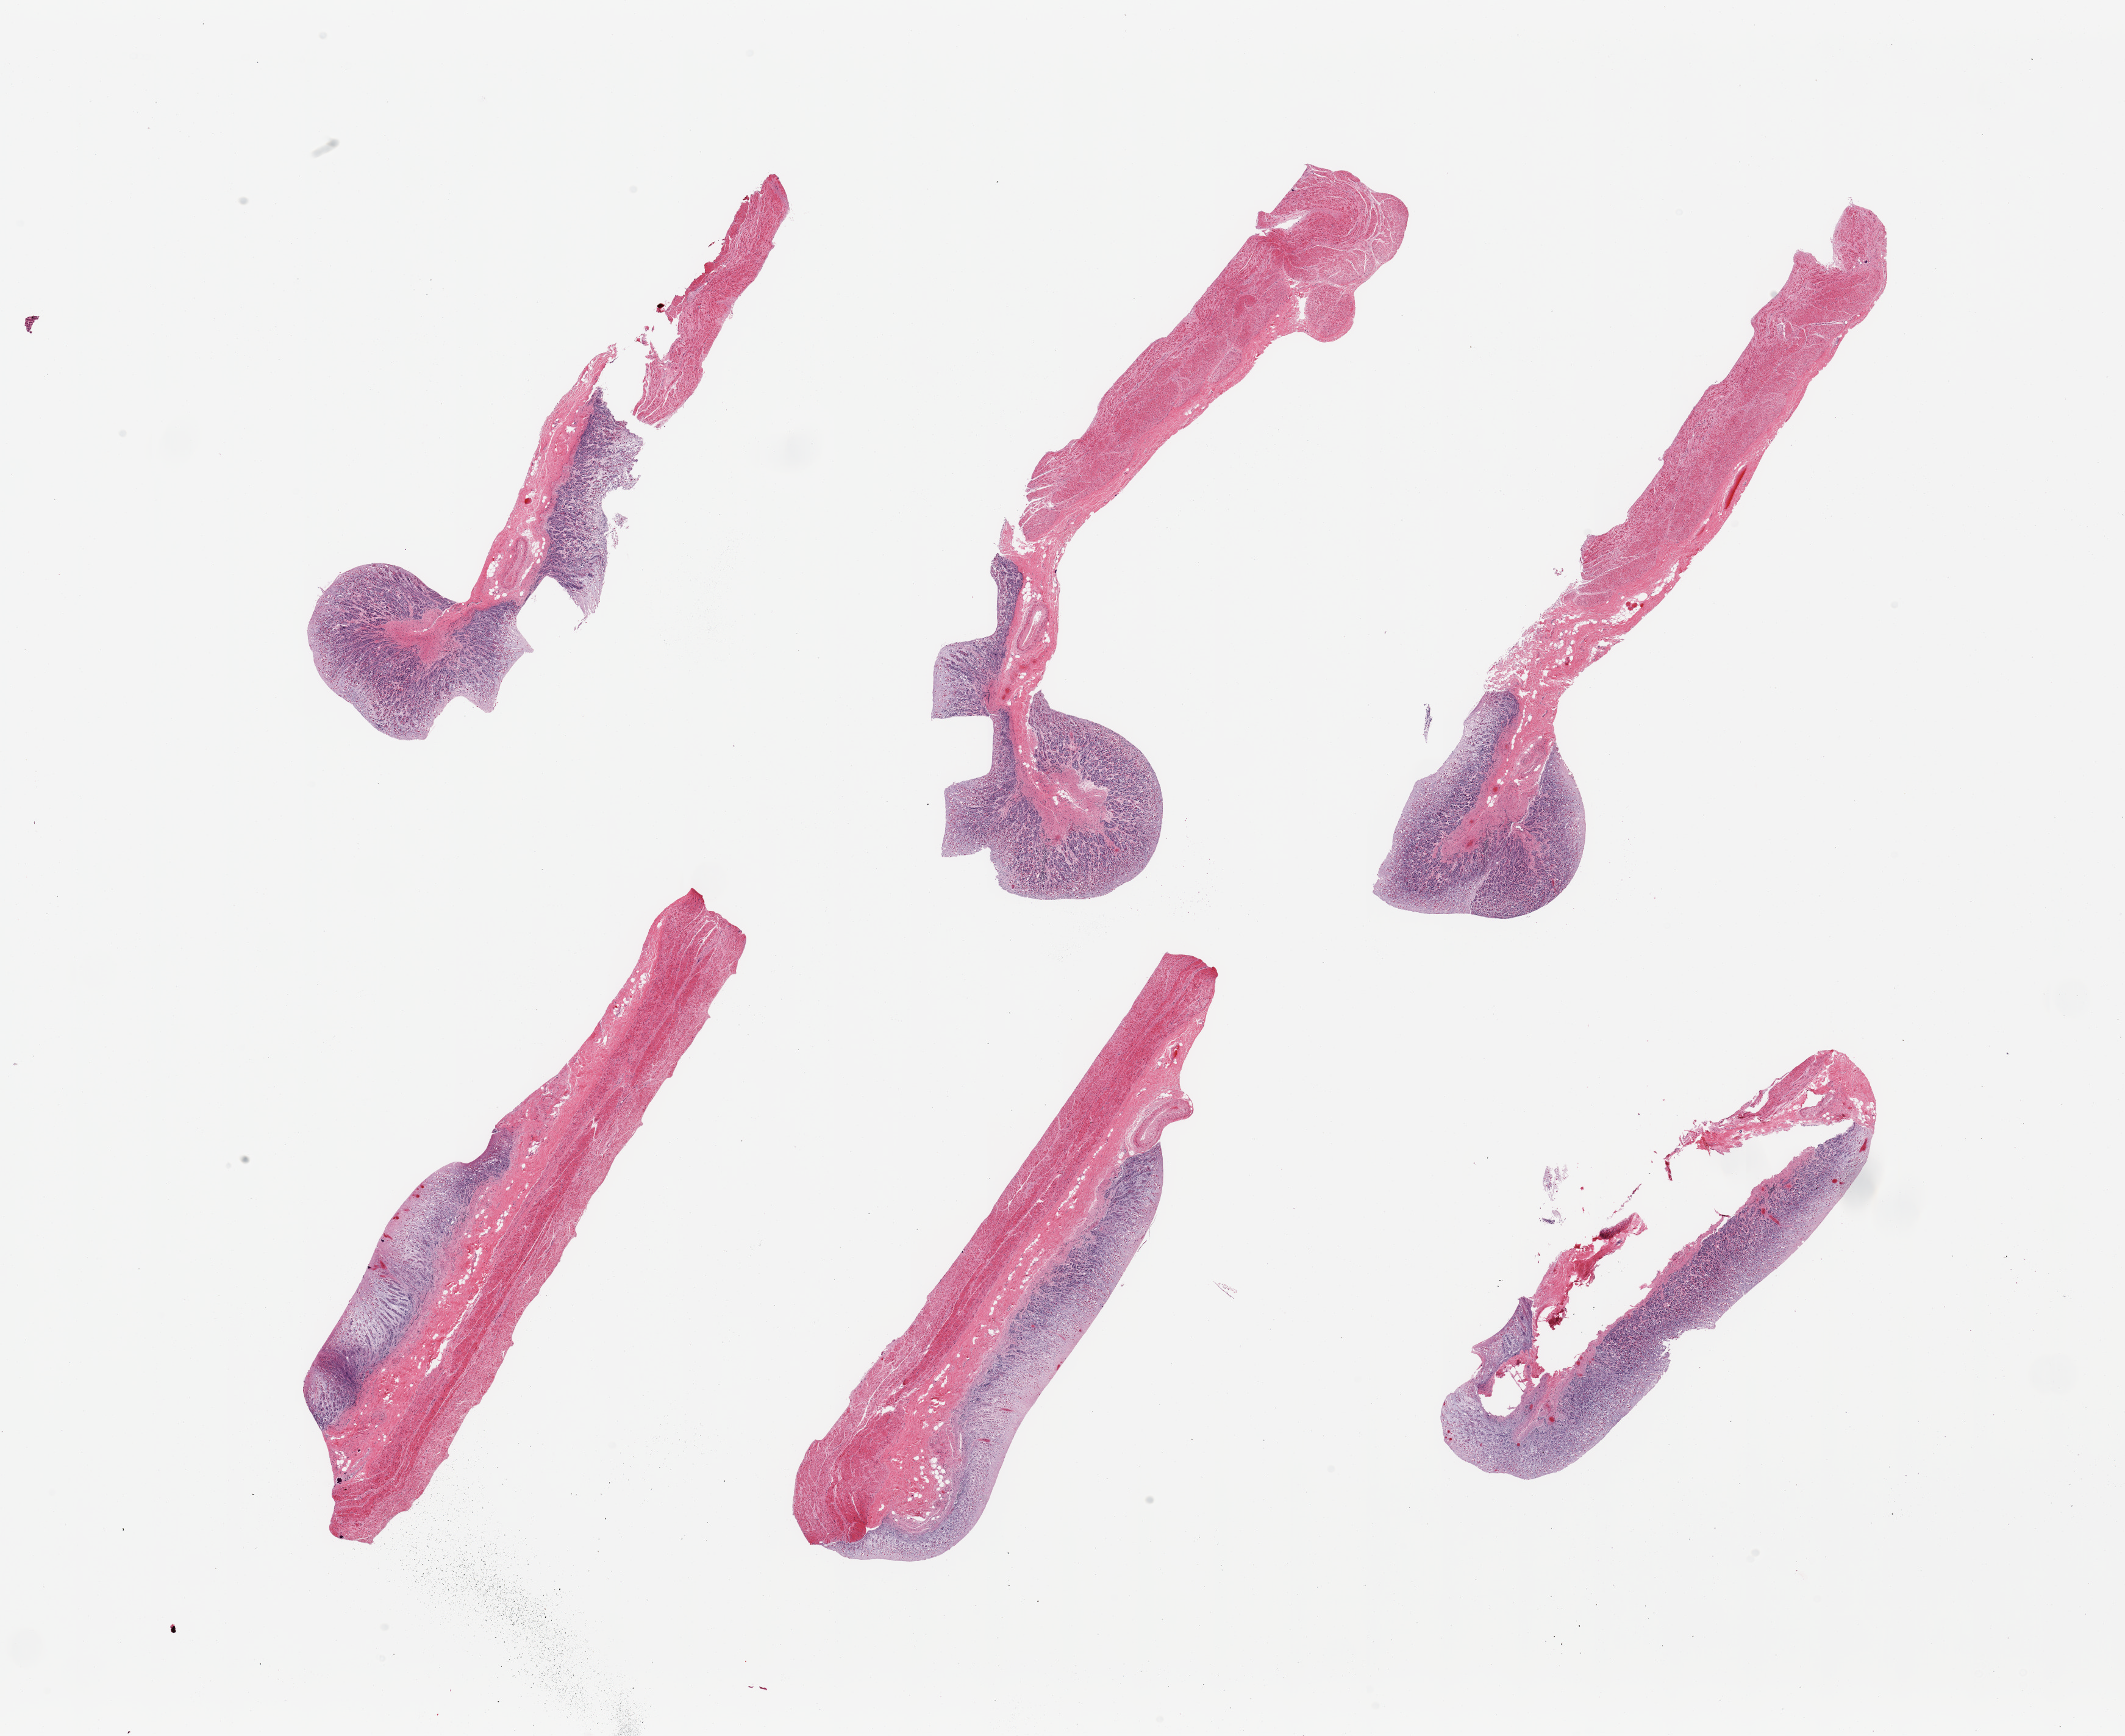
Digitized H&E-stained section, brightfield, low-resolution overview of the scanned area, about 27.6 x 22.5 mm. PAXgene-fixed, paraffin-embedded tissue. Sampled site (target tissue): stomach. Tissue donor sample.
- reviewer comment on this tissue sample: 6 pieces; mucosa is poorly preserved, muscularis better preserved